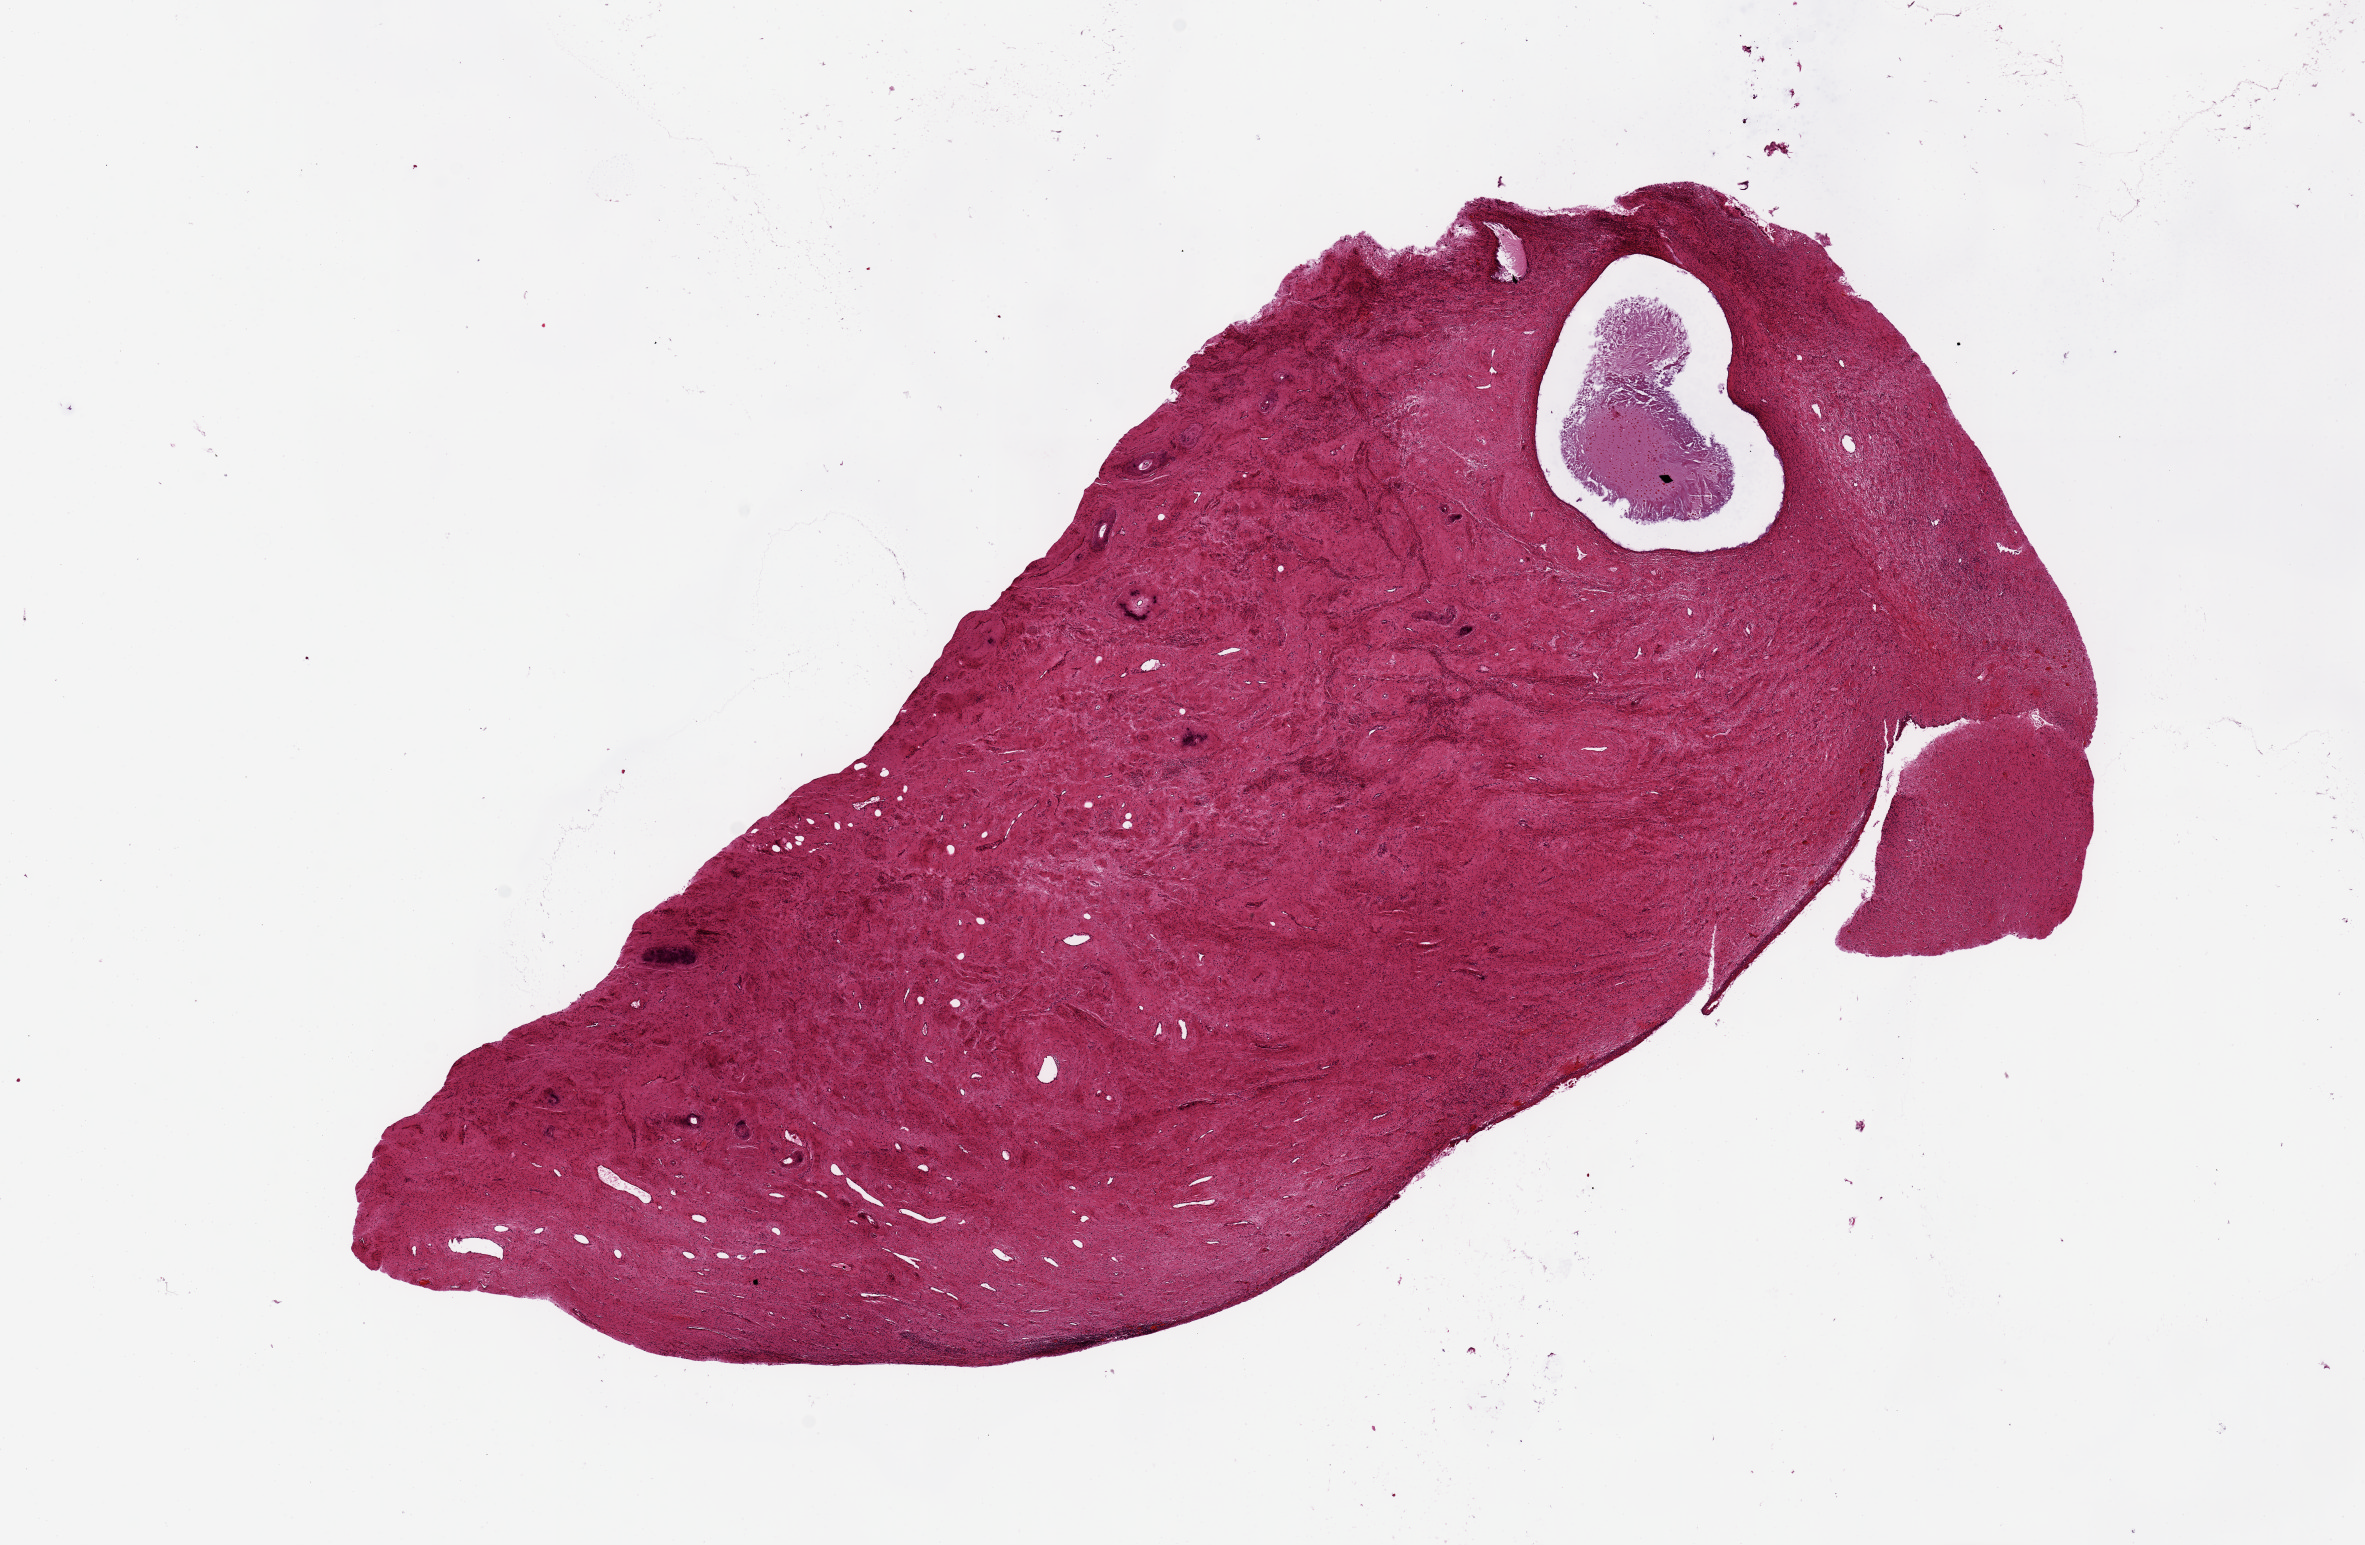
Whole-slide image, haematoxylin and eosin stain, brightfield, whole scanned area (about 18.7 x 12.2 mm) shown as a low-resolution overview; PAXgene-fixed, paraffin-embedded tissue; sampled site (target tissue): exocervix; tissue donor sample. Donor: female.
- reviewer comment on this tissue sample: 14x6 mm; partly sloughed; thin squamous surface; cyst